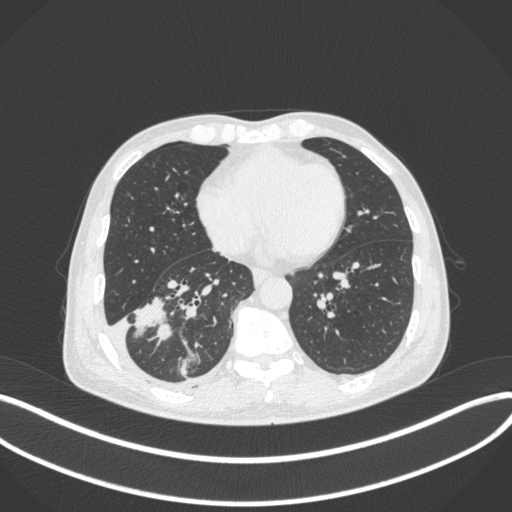
Chest CT, one axial slice. Position 142 of 385 along the scan axis. 120 kVp. Lung window (W 1500 / L -600 HU). 1 mm slice thickness. 512 × 512 image matrix, field of view 400 × 400 mm. Male patient, age 64 years. Case-level facts recorded for this patient, not image findings: clinical TNM (as recorded): T3 N0 M0; histopathological grade: G2-3.
Annotated regions visible in this slice (bounding box drawn by a radiologist):
- lung tumour (recorded histology: adenocarcinoma): box from (x=131, y=297) to (x=173, y=344) px